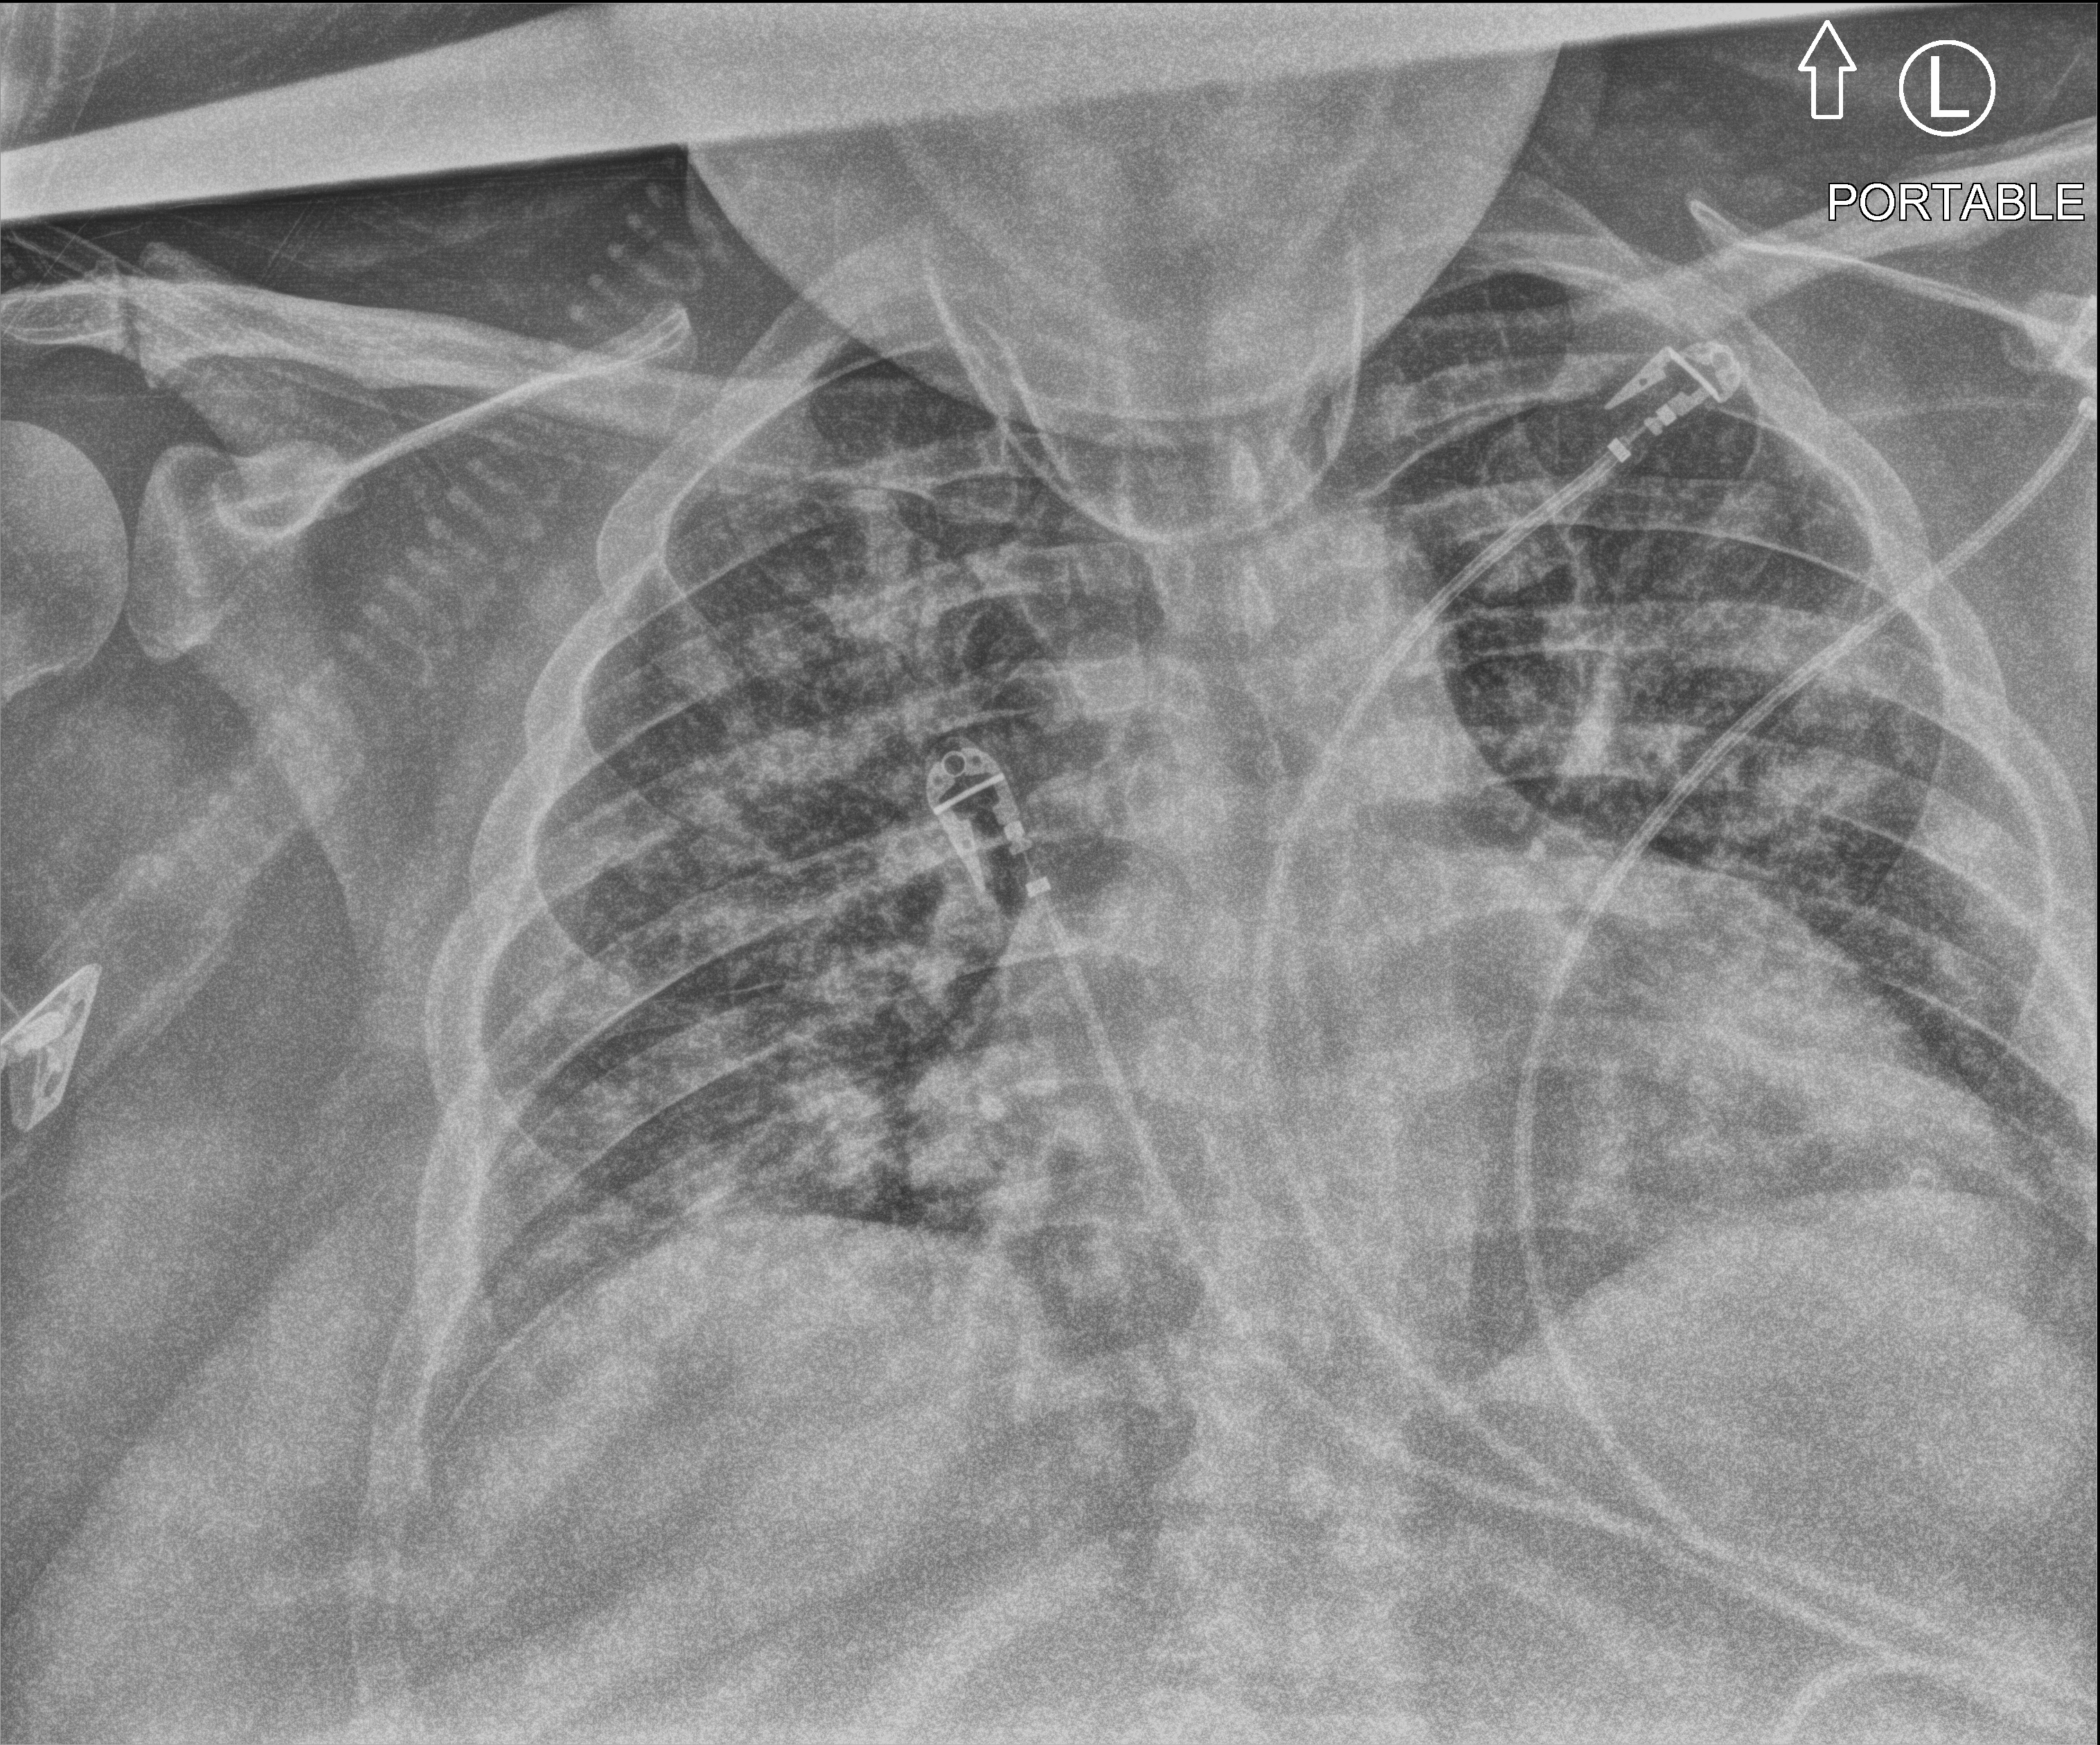
Chest X-ray (portable). Patient hospitalised with COVID-19; male, aged 18–59 years.
Hospital-stay facts (about this admission, not read from this image; timing relative to this image not recorded):
- mechanically ventilated during this hospital stay: no
- admitted to intensive care during this hospital stay: yes